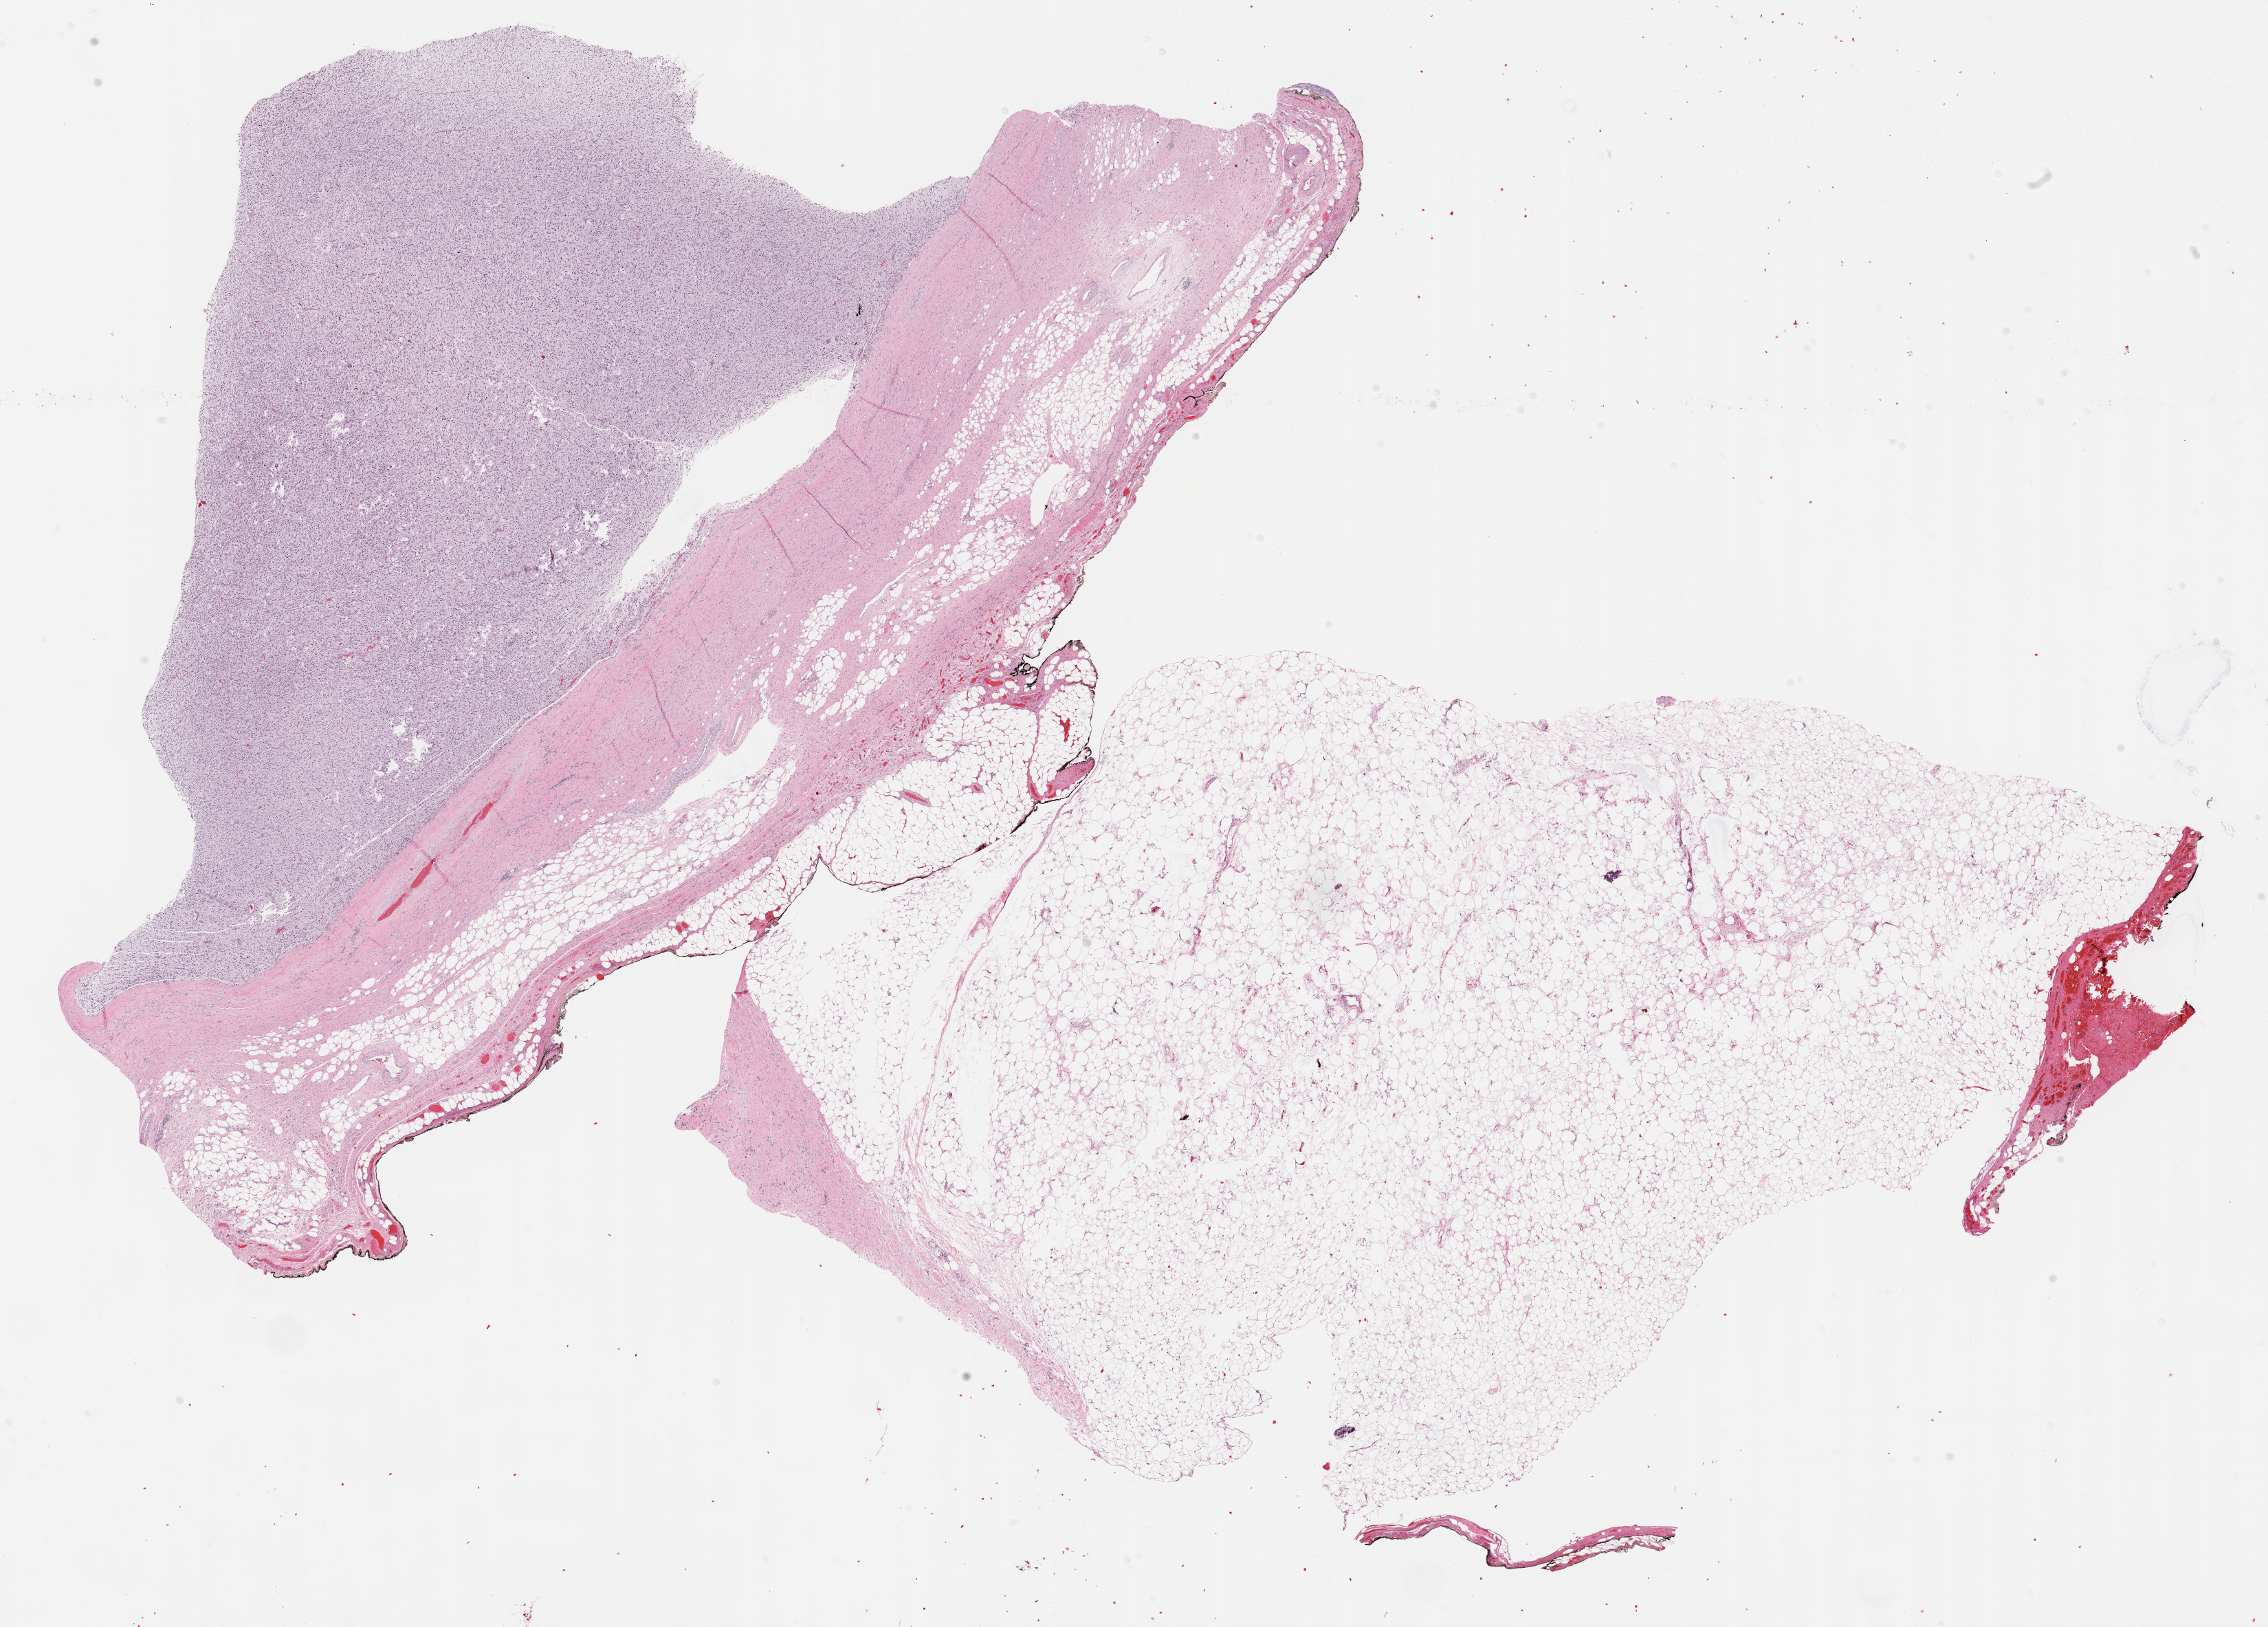
Digitized H&E-stained tissue section (whole slide) — whole scanned area (about 26.7 x 19.1 mm, from a 40x scan) shown as a low-resolution overview; formalin-fixed paraffin-embedded (FFPE) diagnostic section; sample: primary tumour, colon. Patient: male, age at initial diagnosis 65 years.
Diagnosis: Dedifferentiated liposarcoma (descending colon).